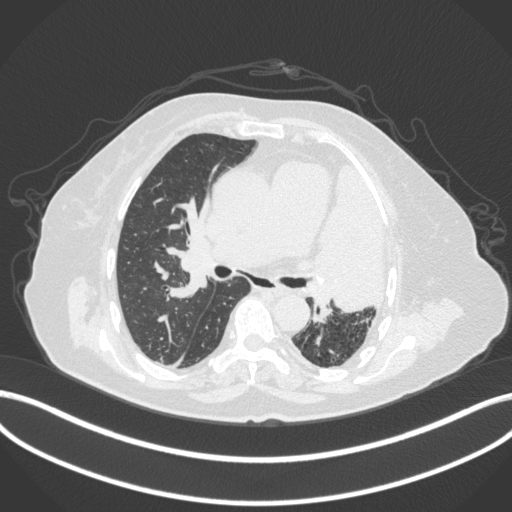
Chest CT, one axial slice. Position 226 of 399 along the scan axis. Lung window (W 1500 / L -600 HU). 1 mm slice thickness. 512 × 512 image matrix. Patient: female, 75 years. Case-level facts recorded for this patient, not image findings: clinical TNM (as recorded): T3 N3 M1.
Outlined on this slice (bounding box drawn by a radiologist):
- lung tumour (recorded histology: adenocarcinoma): box from (x=308, y=157) to (x=386, y=314) px